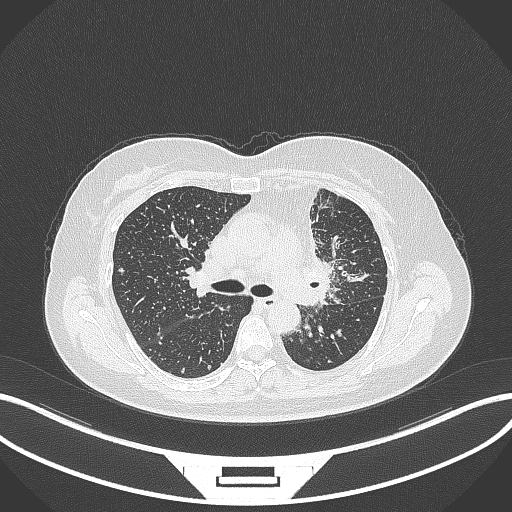
Chest CT, one axial slice. Position 210 of 348 along the scan axis. Lung window (W 1500 / L -600 HU). 512 × 512 image matrix, field of view 400 × 400 mm. Patient: female, 49 years. From the clinical record (not read from this slice): clinical TNM (as recorded): T1c N0 M1.
Outlined on this slice (bounding box drawn by a radiologist):
- lung tumour (recorded histology: adenocarcinoma): box from (x=290, y=253) to (x=337, y=307) px